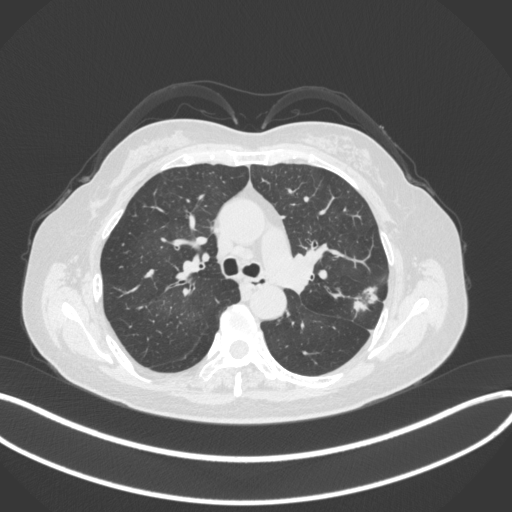
Chest CT, one axial slice; slice 218 of 330 in the series (ordered by position); reconstruction kernel B31f; 120 kVp; lung window (W 1500 / L -600 HU); 512 × 512 image matrix, field of view 400 × 400 mm. Patient: female, 60 years. From the clinical record (not read from this slice): clinical TNM (as recorded): T1c N0 M0.
Outlined on this slice (rectangle marked by the reading radiologist):
- lung tumour (recorded histology: adenocarcinoma): bounding box (x1, y1, x2, y2) in pixels: (348, 275, 382, 318)